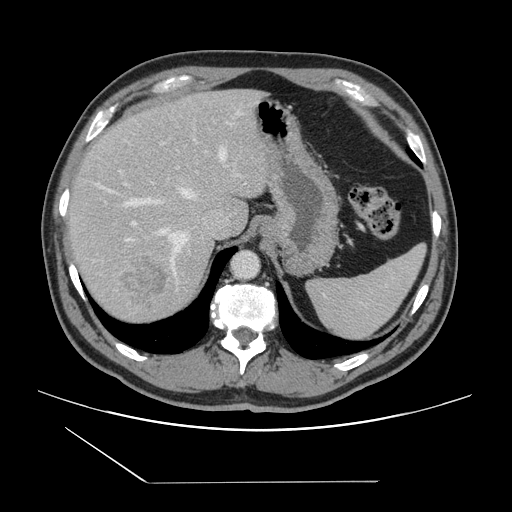
Contrast-enhanced abdominal CT, one axial slice. Slice 112 of 157 in the series (ordered by position). 120 kVp. Intravenous contrast given. Soft-tissue window (W 400 / L 40 HU). 512 × 512 image matrix, field of view 407 × 407 mm. Male patient, age 61 years. Case-level facts recorded for this patient, not image findings: diagnosis: colorectal cancer liver metastases, imaged before liver resection; multiple liver metastases: yes; largest metastasis: 5.5 cm; disease in both lobes: yes.
Outlined on this slice (manually delineated by an expert):
- hepatic veins: bounding box <101,148,226,280> (left, top, right, bottom; pixels)
- liver: <68,90,269,325>
- planned liver remnant (the part of the liver to remain after resection): <69,90,236,231>
- portal vein (with intrahepatic branches): <126,174,241,225>
- liver metastasis: <116,252,171,317>